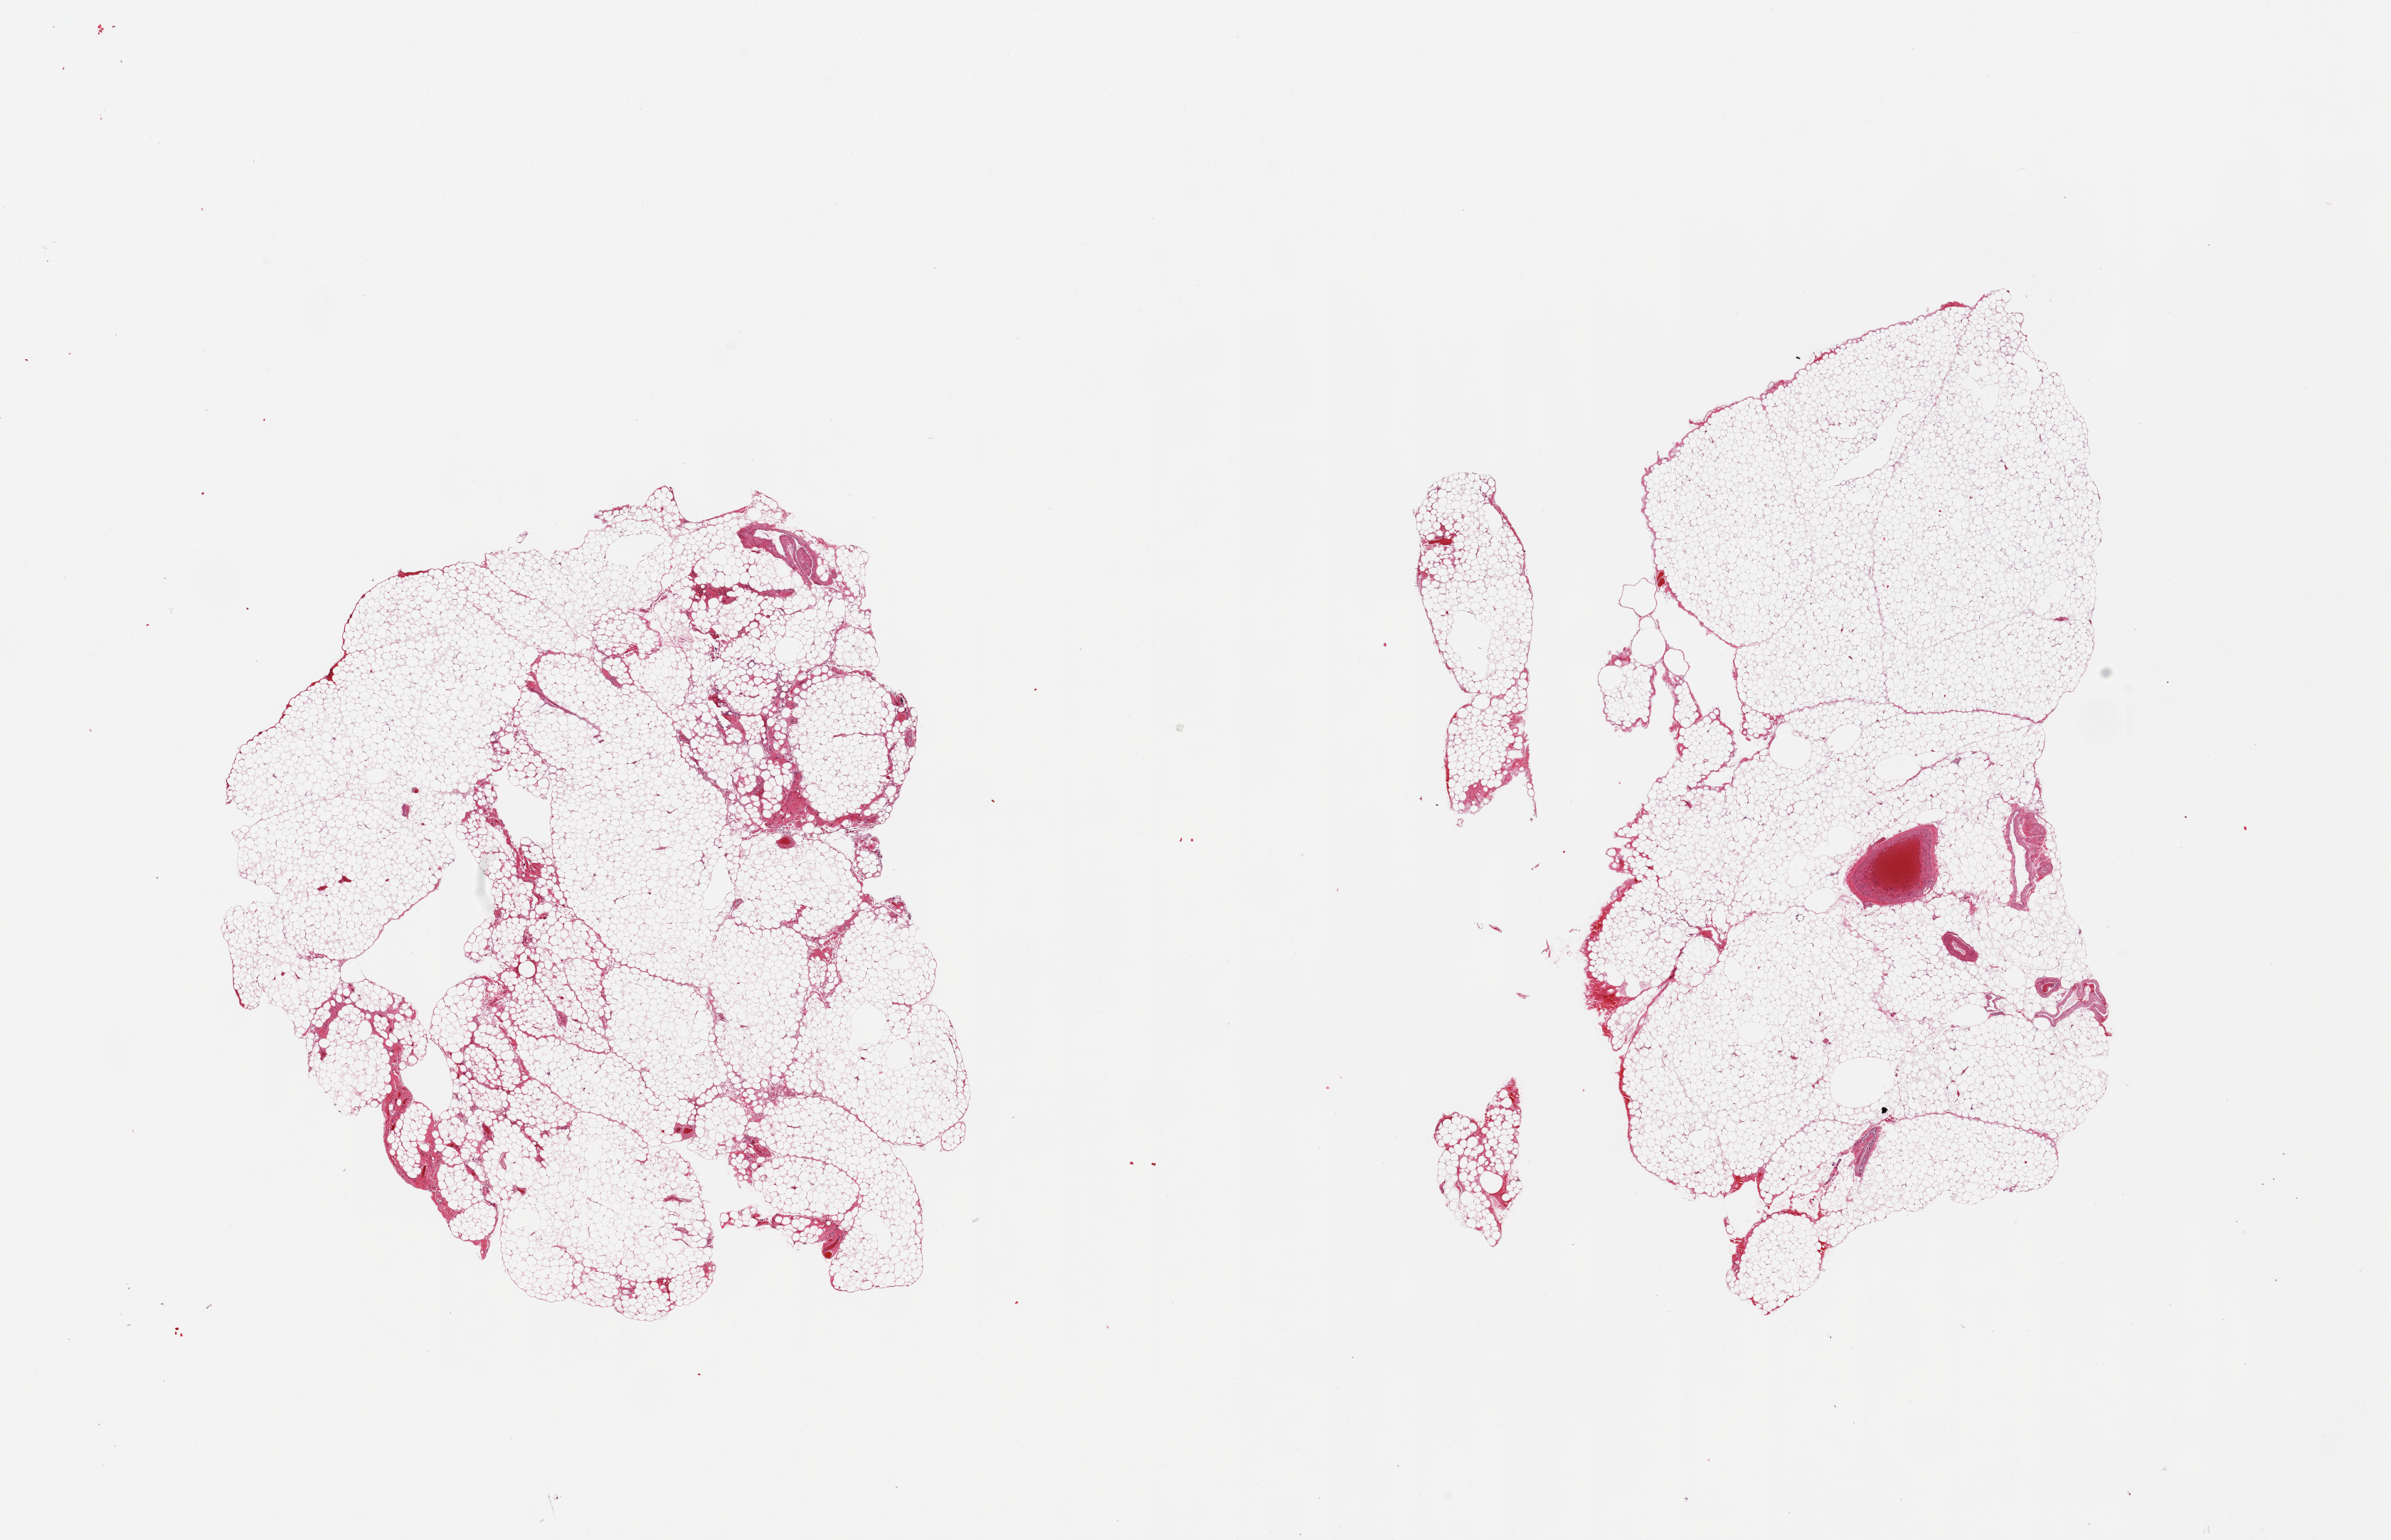
Whole-slide image, hematoxylin and eosin (H&E) stain, a low-resolution overview of the entire scanned area, about 26.6 x 17.1 mm (acquisition: 20x scan). PAXgene-fixed paraffin-embedded (PFPE) section. Target tissue: omentum. Donor tissue sample. Donor: male.
• pathologist's review note for this sample: 2 pieces